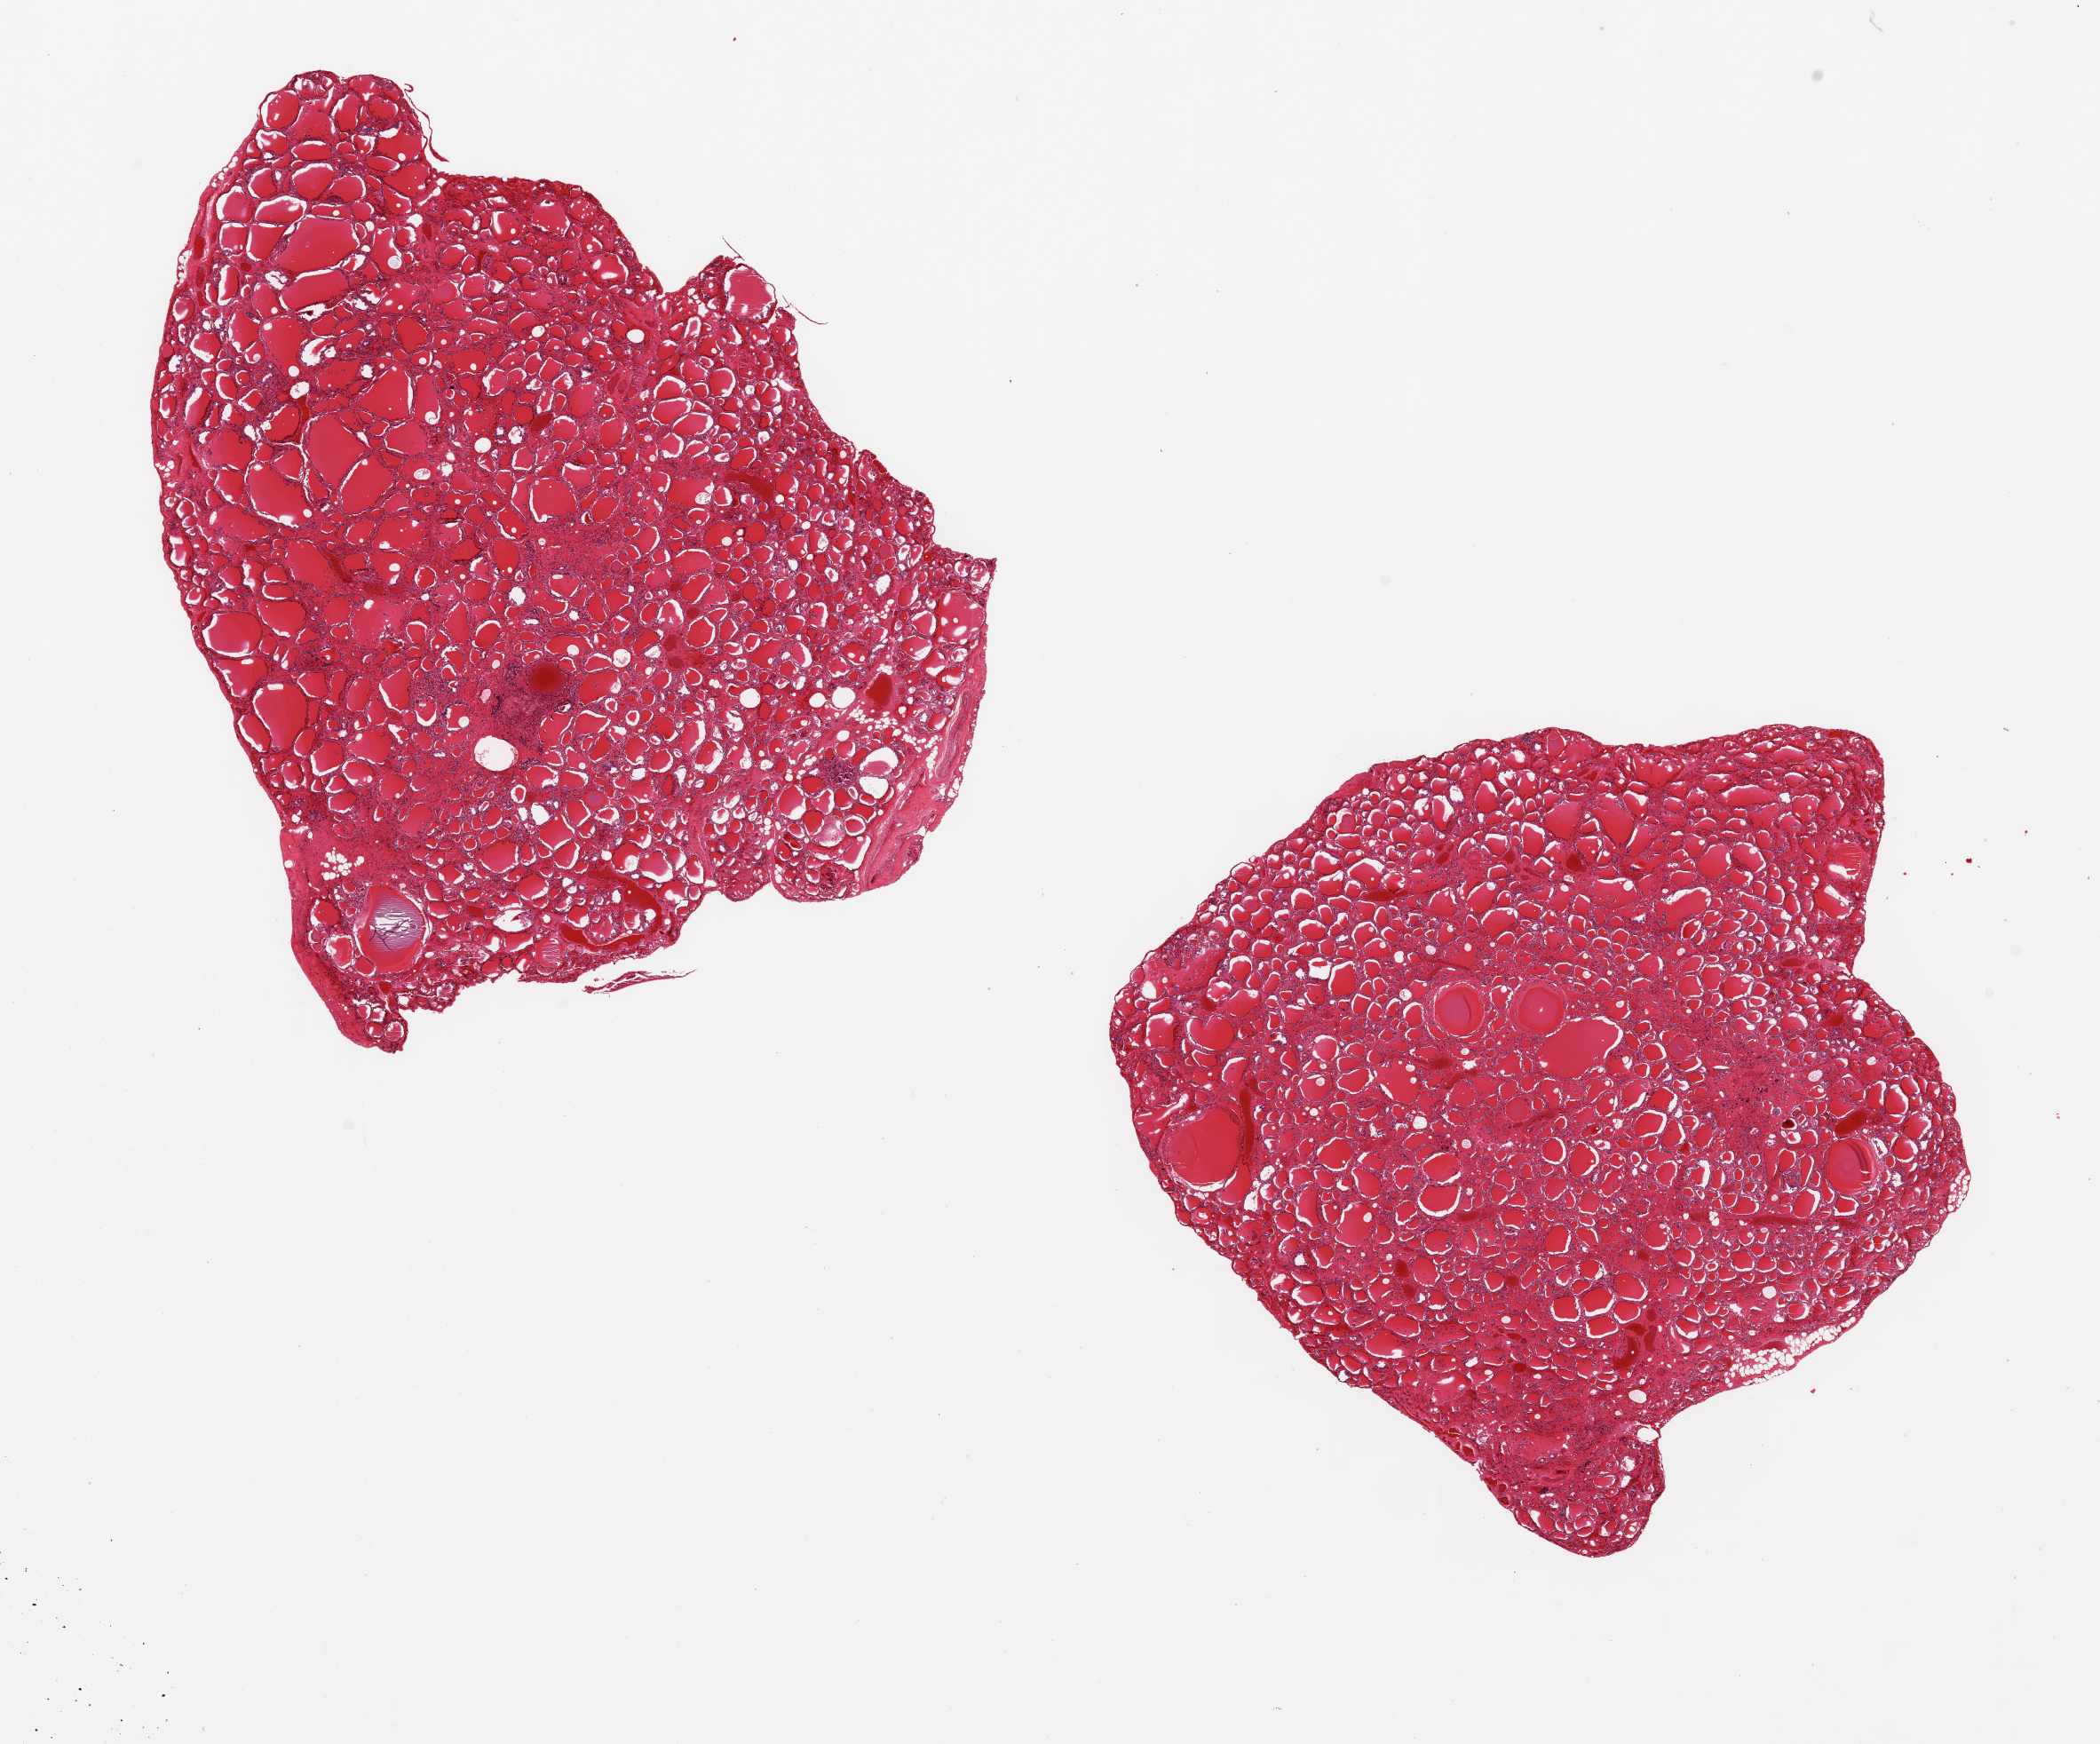
Digitized haematoxylin and eosin-stained section — whole scanned area (about 18.7 x 15.5 mm) shown as a low-resolution overview, PAXgene-fixed, paraffin-embedded tissue, target tissue: thyroid, tissue donor sample.
Reviewer comment on this tissue sample: 2 ~8x6.5mm aliquots.